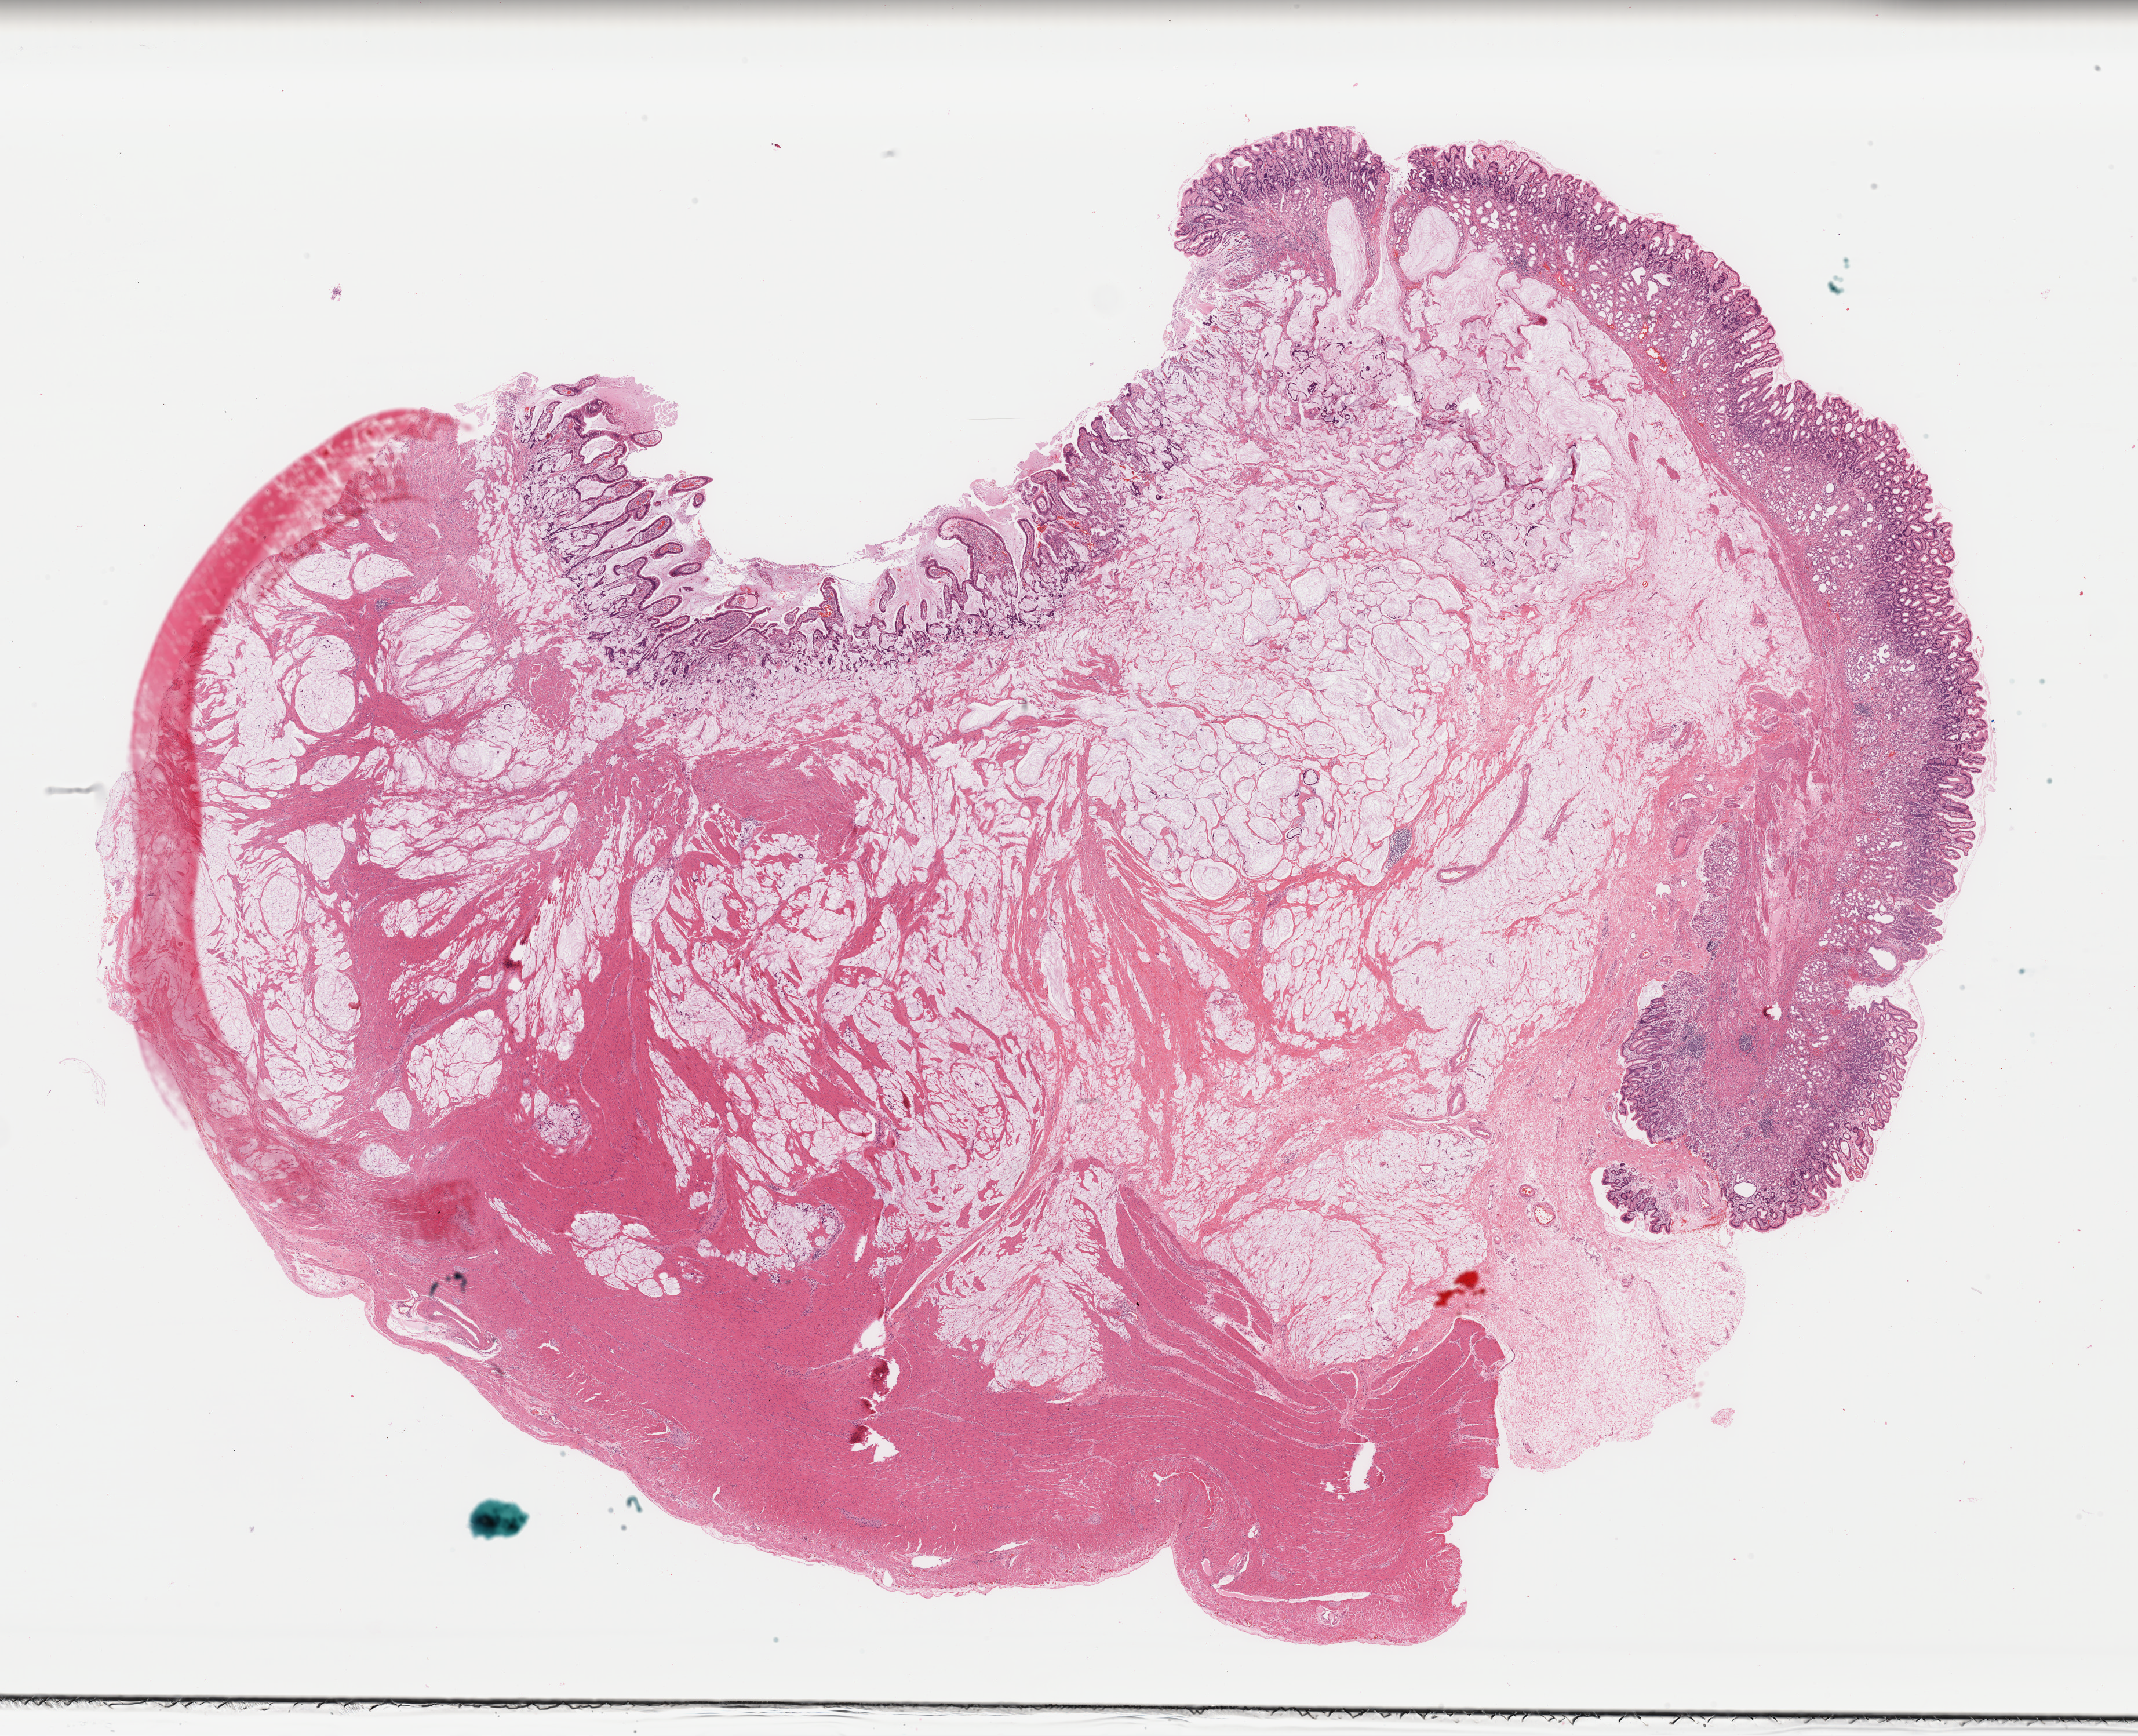
Whole-slide histology image, H&E, a low-resolution overview of the entire scanned area, about 29.1 x 23.7 mm (from a 40x scan); formalin-fixed paraffin-embedded (FFPE) diagnostic section; sample: primary tumour, stomach. Male, age 56 years at initial diagnosis. Histologic grade: G3 (poorly differentiated).
Pathologic diagnosis: Mucinous adenocarcinoma (gastric antrum). AJCC pathologic stage: IIIA (7th edition). Lymph nodes positive (case pathology): 1 of 5 examined.